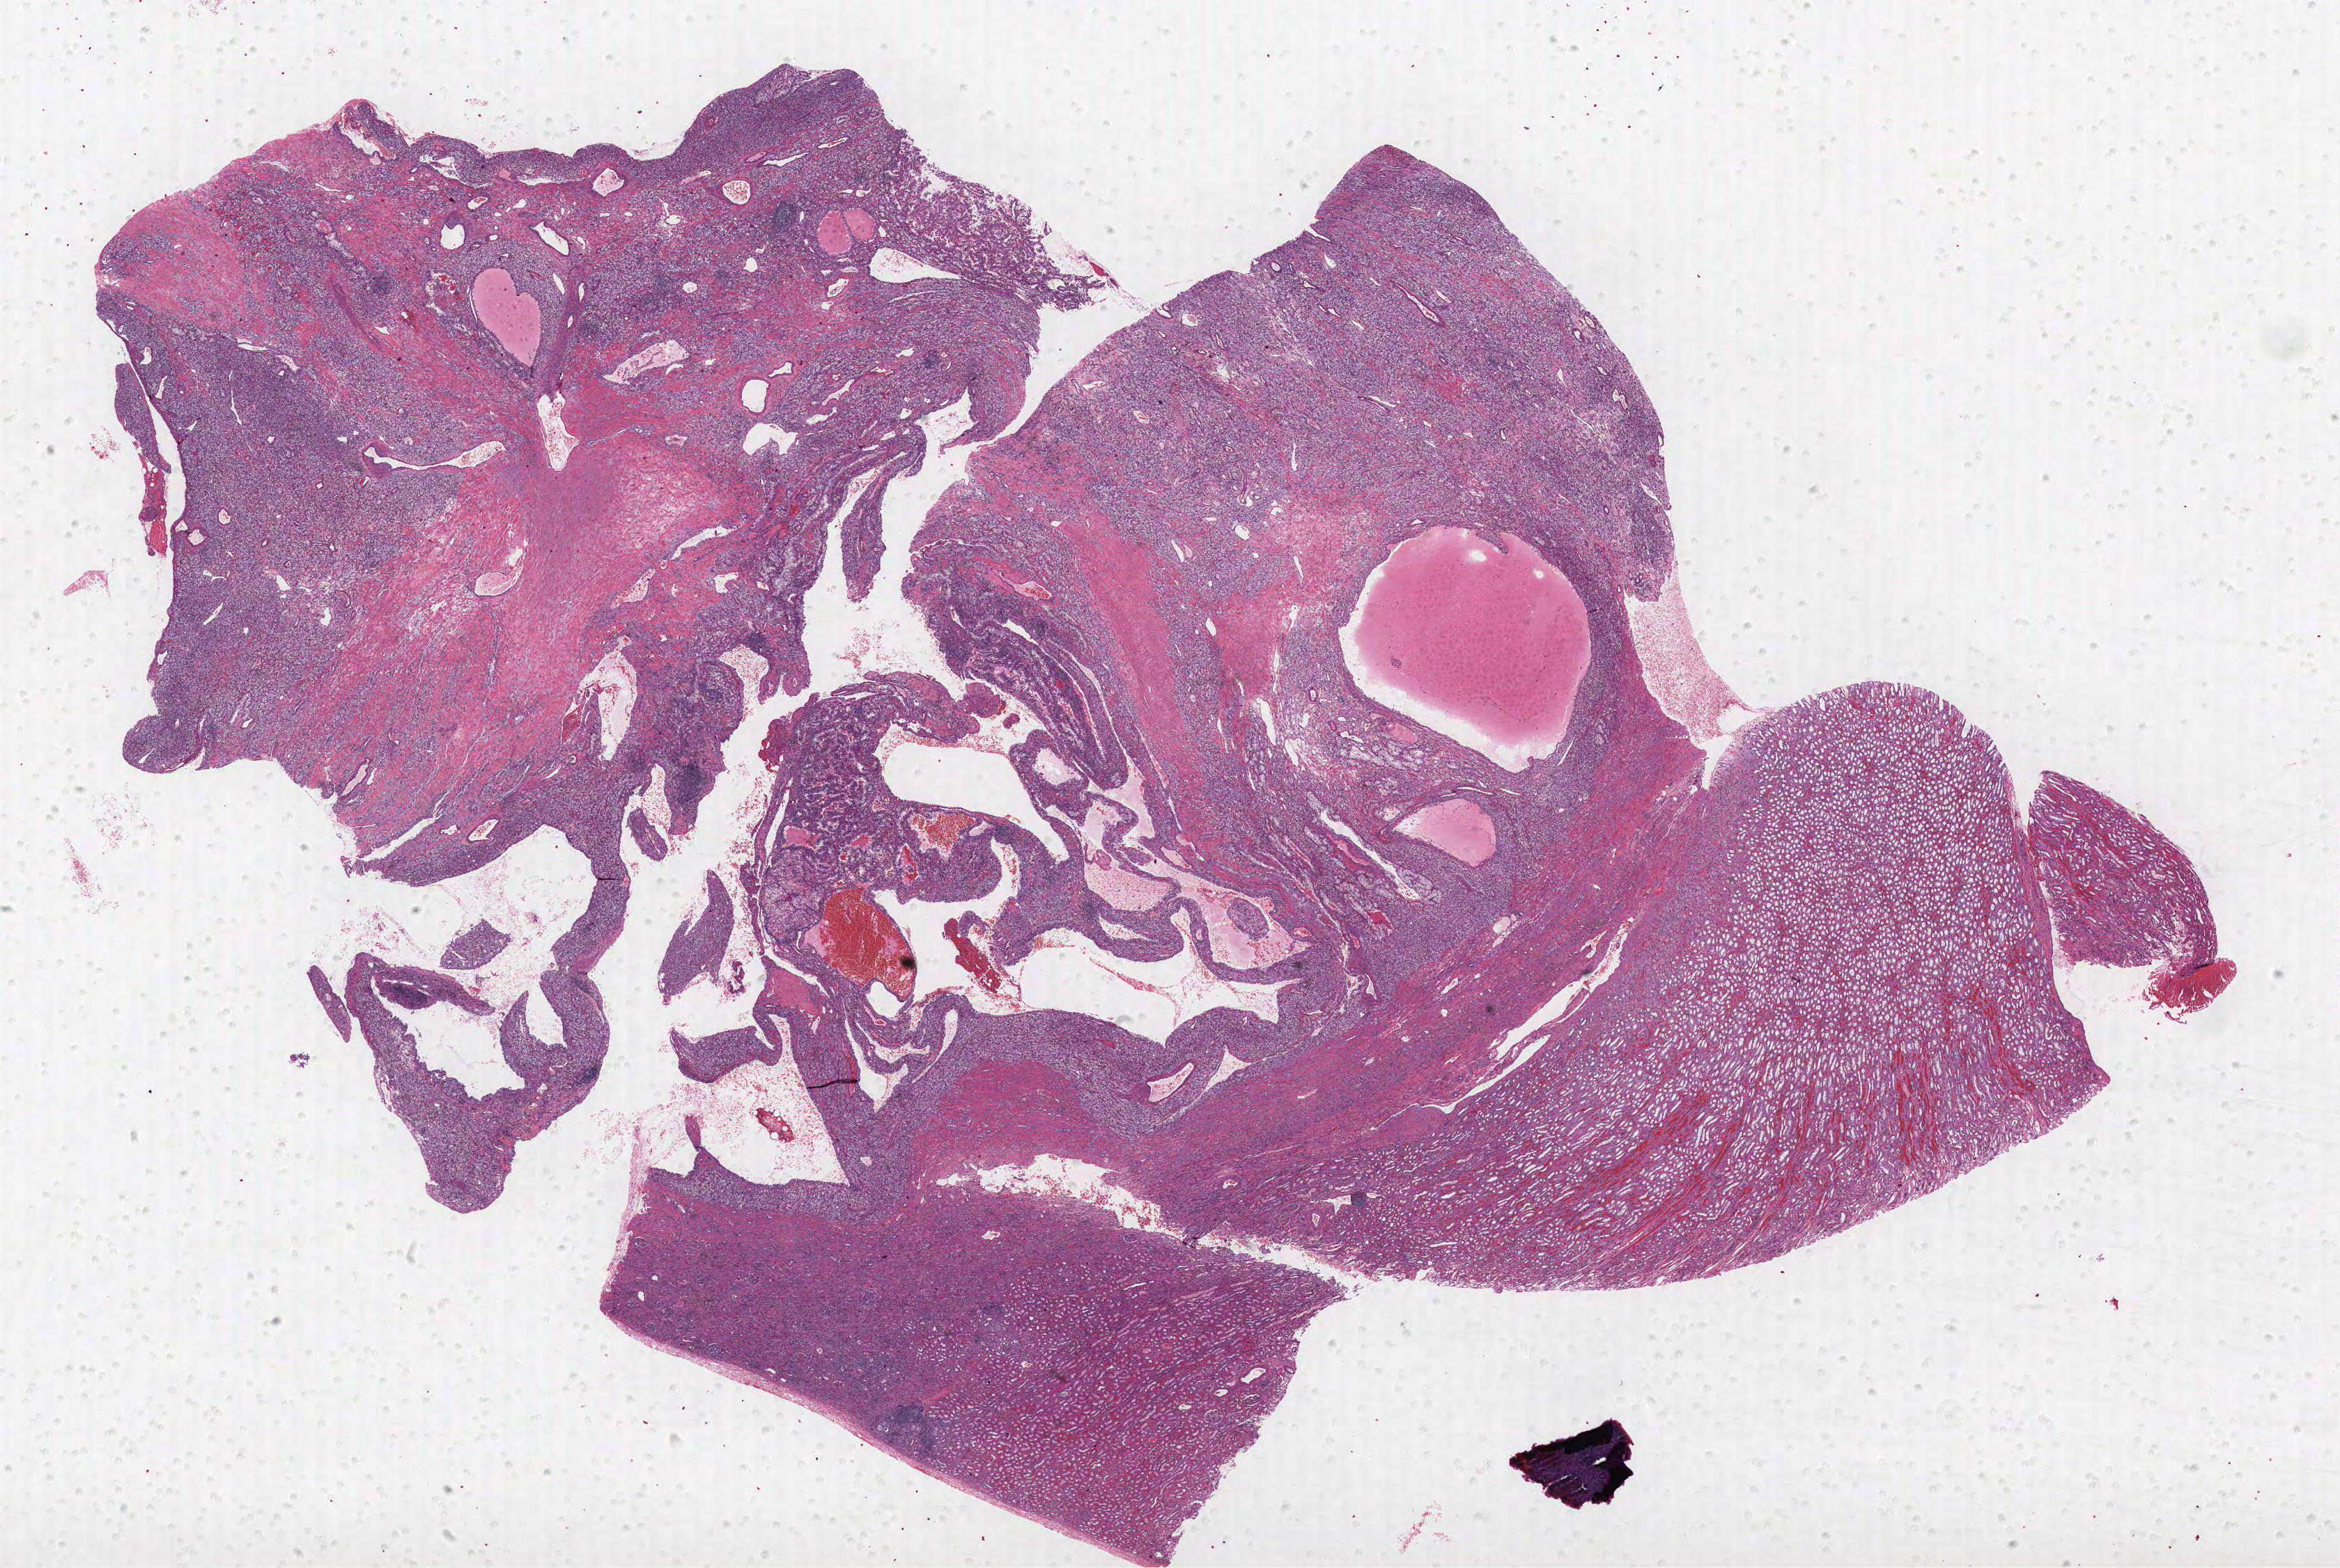
Whole-slide histology image, H&E, shown as a low-resolution overview of the whole scanned area (about 26.9 x 18.0 mm, acquisition: 40x scan). Formalin-fixed paraffin-embedded (FFPE) diagnostic section. Primary tumour sample from the kidney. Male, age 44 years at initial diagnosis. Histologic grade: G3 (poorly differentiated).
Diagnosis: Clear cell adenocarcinoma, NOS. Lymph nodes positive (case pathology): 2 of 2 examined. AJCC pathologic stage: III.